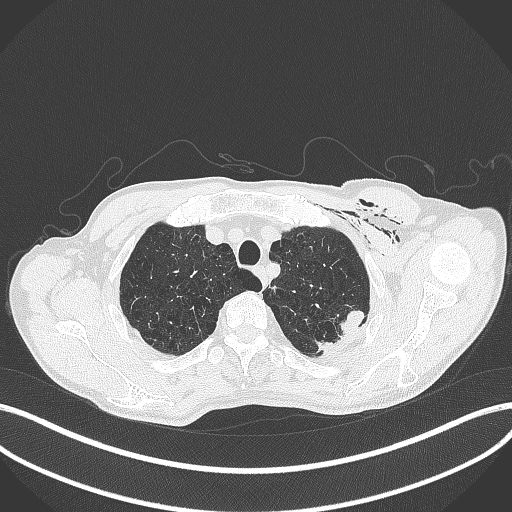
Chest CT, one axial slice; position 355 of 457 along the scan axis; reconstruction kernel B70f; 120 kVp; lung window (W 1500 / L -600 HU); 512 × 512 image matrix. Patient: male, 58 years. Case-level facts recorded for this patient, not image findings: clinical TNM (as recorded): T3 N0 M0.
Annotated regions visible in this slice (rectangle marked by the reading radiologist):
- lung tumour (recorded histology: adenocarcinoma): bounding box (x1, y1, x2, y2) in pixels: (312, 310, 371, 355)